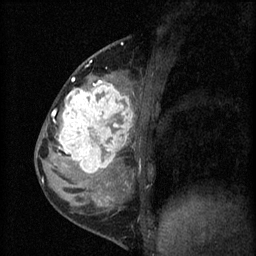
Breast MRI (dynamic contrast-enhanced), one sagittal slice; slice 23 of 60 in the series (ordered by position); 3 images stored at this slice position (order not interpretable as contrast timing); 1.5 T; TE 4.2 ms, TR 8.2 ms; 2 mm slice thickness; 256 × 256 image matrix. Patient: female, 37 years.
Outlined on this slice (semi-automatic segmentation, software-assisted and operator-edited):
- analysis volume of interest (the breast-tissue region the enhancement analysis was run in; not a lesion): box from (x=53, y=78) to (x=140, y=181) px
- tumour enhancement mask (voxels above the 70 % enhancement threshold inside the analysis volume of interest): (x=53, y=78)–(x=133, y=173)